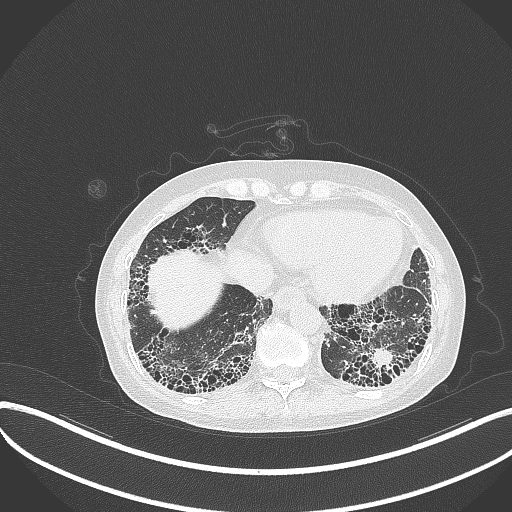
Chest CT, one axial slice; position 70 of 373 along the scan axis; reconstruction kernel B70f; 120 kVp; lung window (W 1500 / L -600 HU); 1 mm slice thickness; 512 × 512 image matrix, field of view 400 × 400 mm. Female patient, age 56 years. Case-level facts recorded for this patient, not image findings: clinical TNM (as recorded): T1 N0 M0.
Annotated regions visible in this slice (rectangle marked by the reading radiologist):
- lung tumour (recorded histology: adenocarcinoma): bounding box (x1, y1, x2, y2) in pixels: (366, 347, 396, 371)